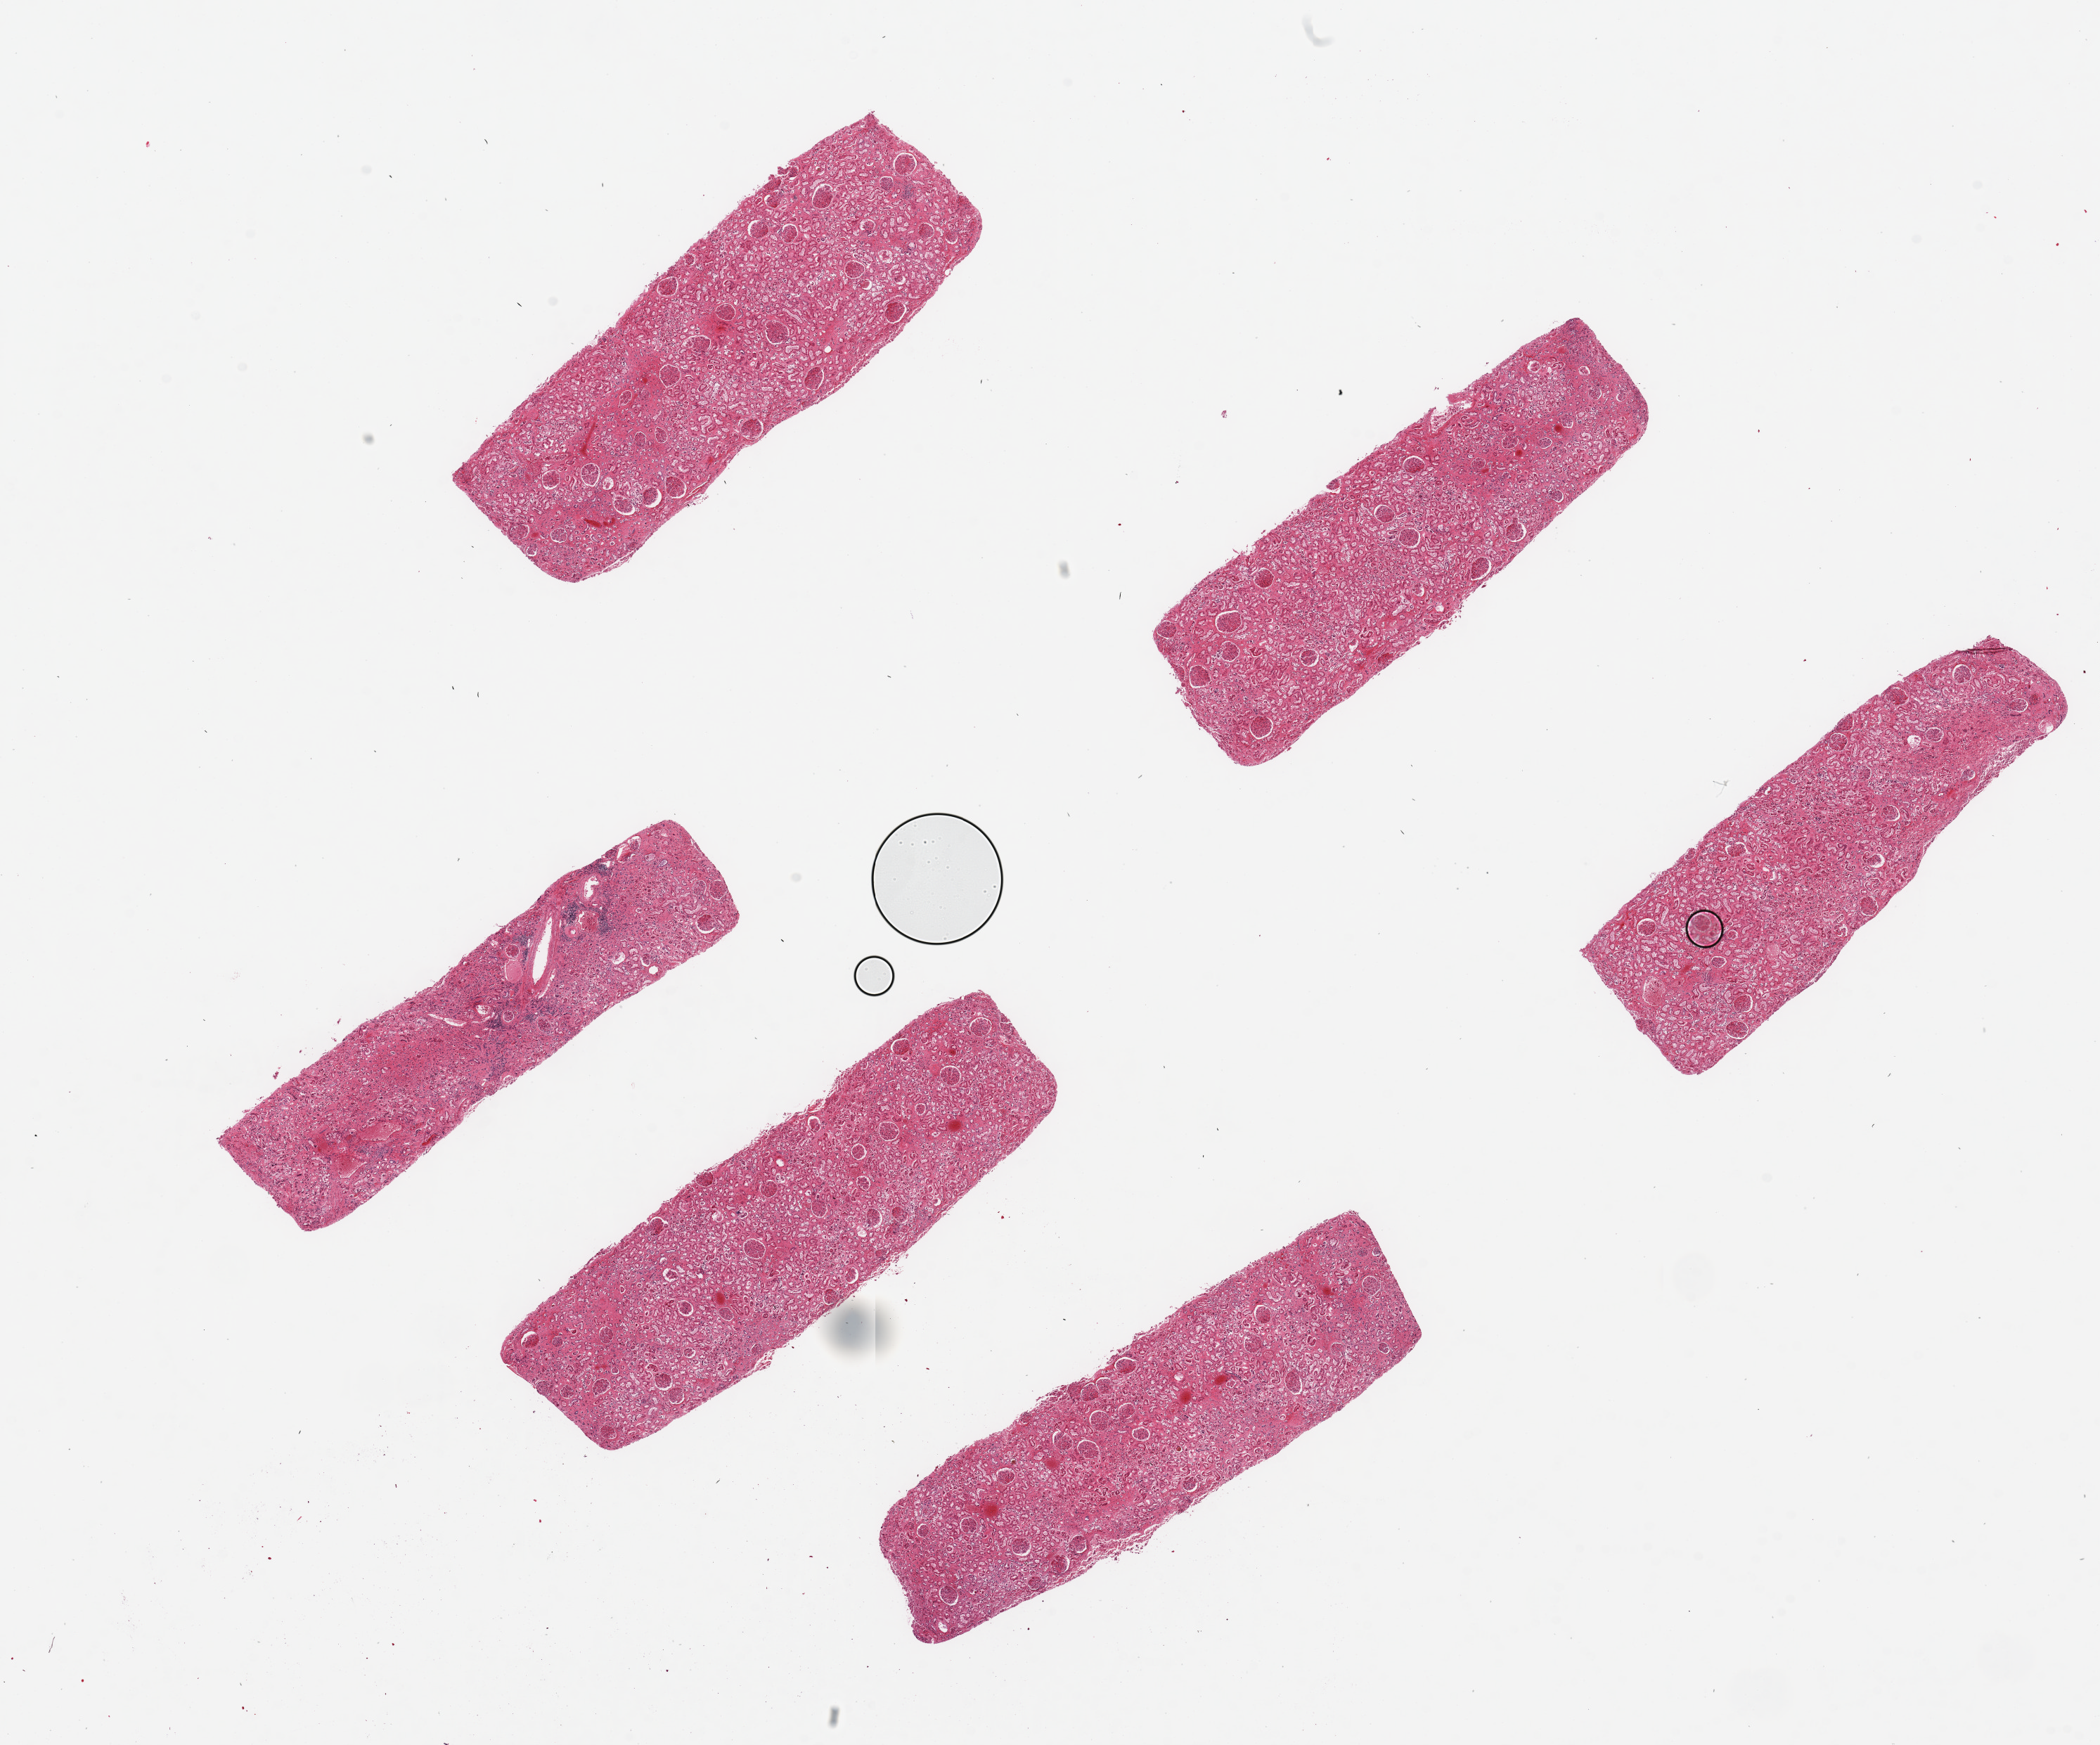
Digitized haematoxylin and eosin-stained section, whole scanned area (about 23.6 x 19.6 mm, acquisition: 20x scan) shown as a low-resolution overview. PAXgene-fixed, paraffin-embedded tissue. Section of renal cortex (target tissue). Tissue donor sample. Donor: male.
- pathologist's review note for this sample: 6 pieces, up to 7x2mm; patchy interstitial fibrosis